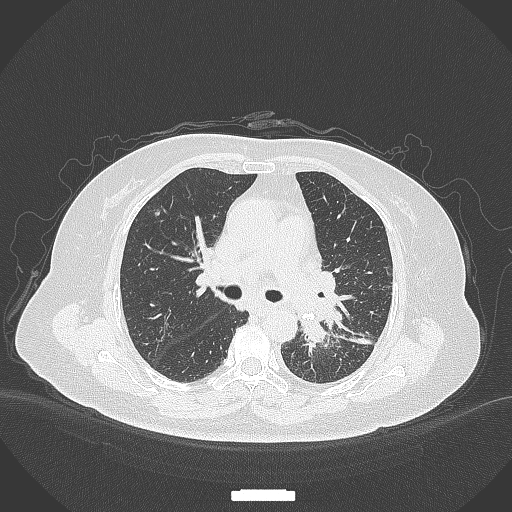
Chest CT, one axial slice; reconstruction kernel B70f; lung window (W 1500 / L -600 HU); 512 × 512 image matrix, field of view 400 × 400 mm. Patient: female, 69 years. From the clinical record (not read from this slice): clinical TNM (as recorded): T2b N3 M1.
Structures marked on this image (bounding box drawn by a radiologist):
- lung tumour (recorded histology: adenocarcinoma): box from (x=297, y=318) to (x=330, y=353) px